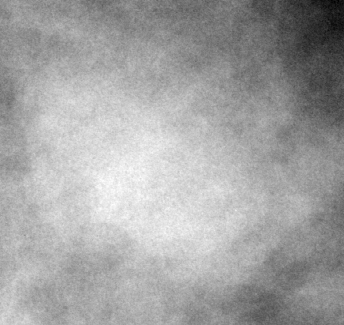
Cropped region of a digitized screen-film mammogram centred on a radiologist-marked abnormality, right breast, MLO view, BI-RADS breast density category 3 (scale 1–4).
Mass, shape oval, margins microlobulated; BI-RADS assessment category 4; pathology result (as recorded, not read from the image): benign.